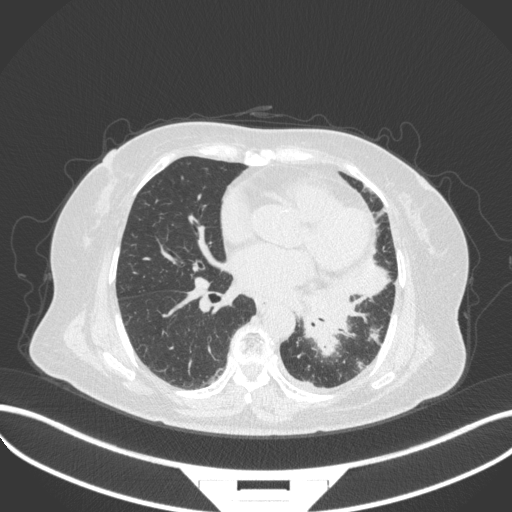
Chest CT, one axial slice. Position 159 of 328 along the scan axis. 120 kVp. Lung window (W 1500 / L -600 HU). 1 mm slice thickness. 512 × 512 image matrix, field of view 400 × 400 mm. Female patient, age 69 years. From the clinical record (not read from this slice): clinical TNM (as recorded): T2b N3 M1.
Annotated regions visible in this slice (bounding box drawn by a radiologist):
- lung tumour (recorded histology: adenocarcinoma): bounding box (x1, y1, x2, y2) in pixels: (290, 278, 351, 362)